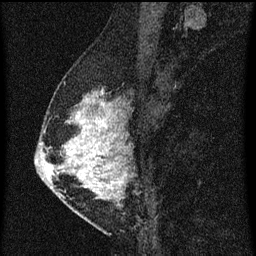
Breast MRI (dynamic contrast-enhanced), one sagittal slice. Dynamic contrast-enhanced series, image 2 of 3 at this slice position (ordered by acquisition). 1.5 T. TE 4.2 ms, TR 8 ms. 2 mm slice thickness. 256 × 256 image matrix. Patient: female, 47 years.
Outlined on this slice (semi-automatic segmentation, software-assisted and operator-edited):
- analysis volume of interest (the breast-tissue region the enhancement analysis was run in; not a lesion): bounding box [x1, y1, x2, y2] px = [50, 80, 139, 203]
- tumour enhancement mask (voxels above the 70 % enhancement threshold inside the analysis volume of interest): [60, 92, 128, 199]